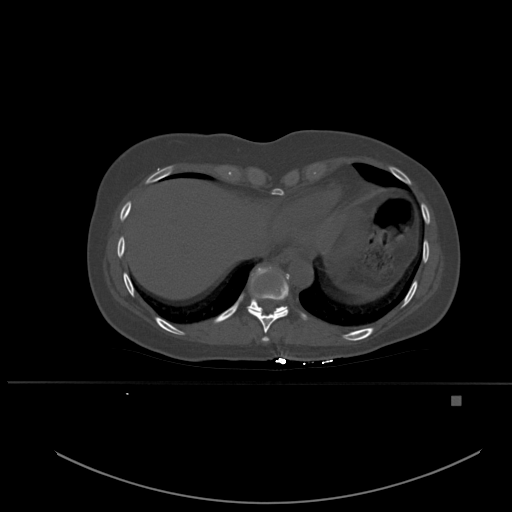
CT including the spine, one axial slice; position 300 of 651 along the scan axis; bone window (W 1800 / L 400 HU); 1.5 mm slice thickness; 512 × 512 image matrix. Patient: female, 49 years. From the clinical record (not read from this slice): primary cancer: breast; vertebrae with lytic lesions (as recorded): L3, T12, L4.
Structures marked on this image (semi-automatically segmented with operator editing):
- T10 vertebra: box from (x=249, y=267) to (x=287, y=313) px
- T8 vertebra: (x=262, y=337)–(x=269, y=342)
- T9 vertebra: (x=247, y=273)–(x=290, y=333)